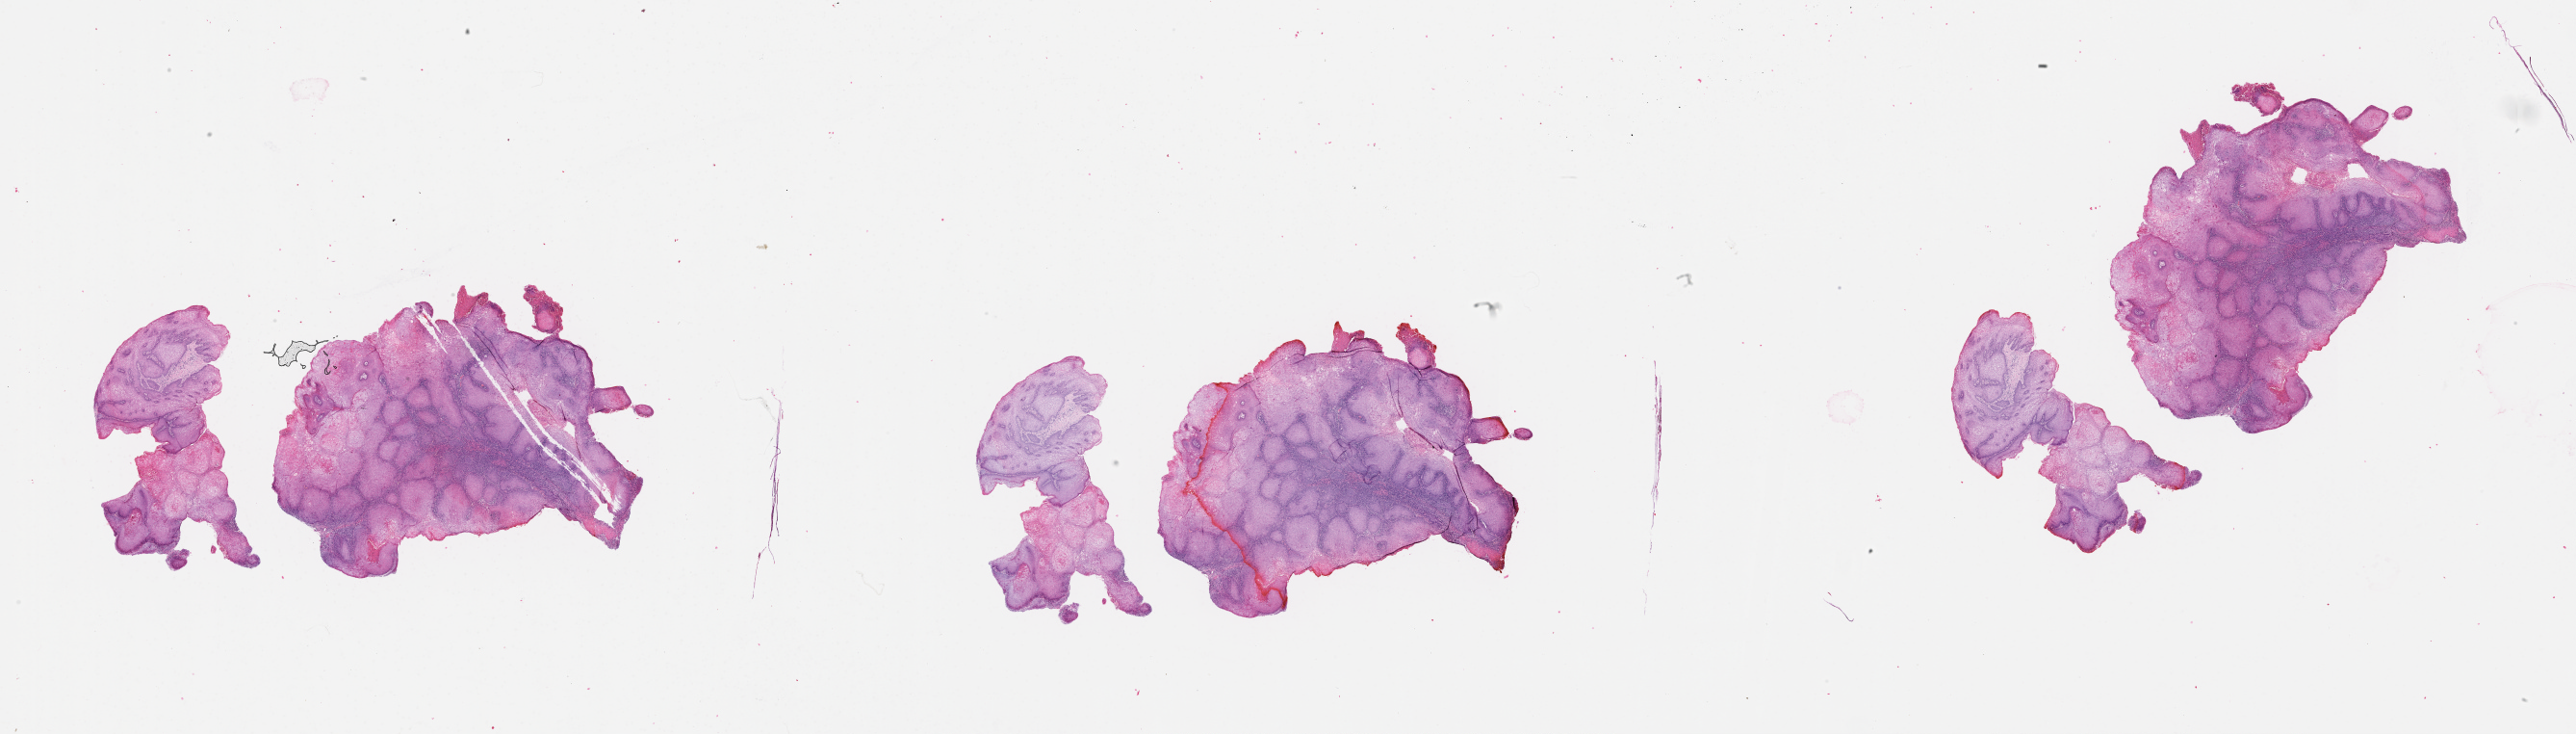
Hematoxylin and eosin (H&E) stained whole-slide image — shown as a low-resolution overview of the whole scanned area (about 43.1 x 12.3 mm). Head and neck, tissue type not recorded. 69-year-old male patient.
Patient diagnosis: Squamous cell carcinoma, NOS (cheek mucosa).